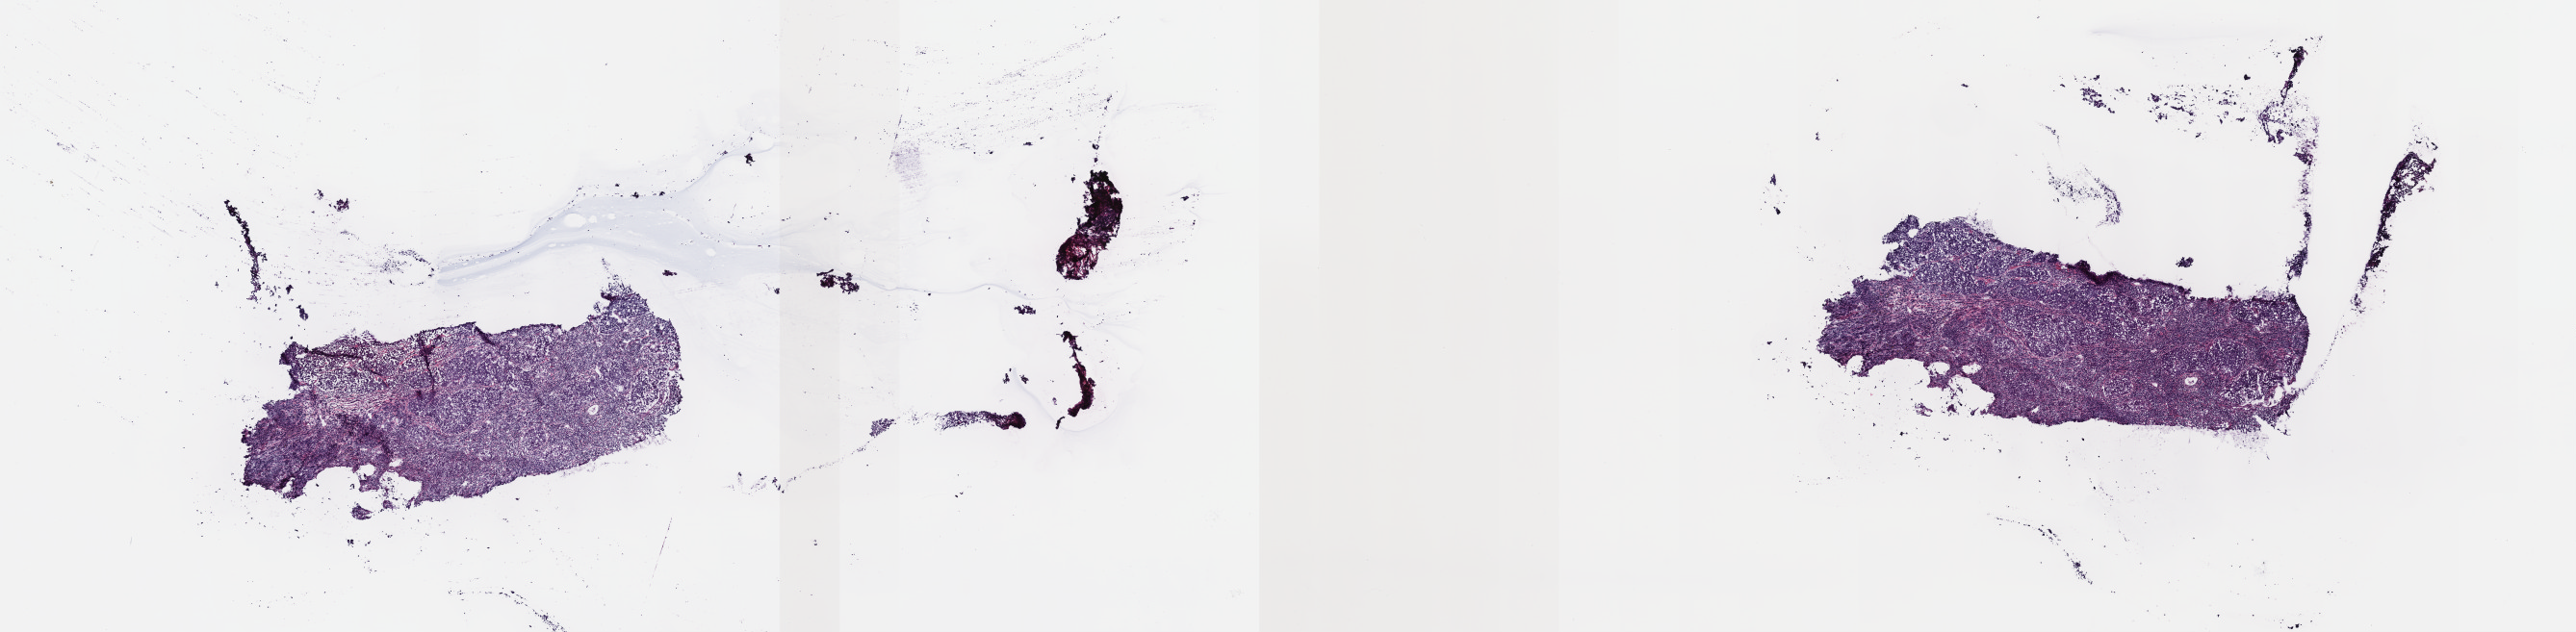
H&E whole-slide image — a low-resolution overview of the entire scanned area, about 21.6 x 5.3 mm, frozen section from the top of the tissue portion, thymus, primary tumour sample. Patient: female, age at initial diagnosis 65 years. Pathologist review of this section (percent, as recorded): tumour cells 100%, tumour nuclei 75%, normal cells 0%, stromal cells 0%, necrosis 0%. Inflammatory infiltration, as recorded: lymphocyte infiltration 5%, monocyte infiltration 0%, neutrophil infiltration 0%.
- histologic diagnosis: Thymic carcinoma, NOS